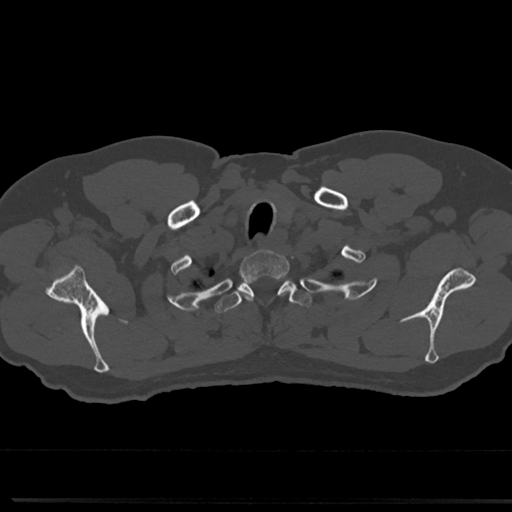
CT including the spine, one axial slice. Slice 651 of 817 in the series (ordered by position). Bone window (W 1800 / L 400 HU). 0.5 mm slice thickness. 512 × 512 image matrix. Patient: male, 61 years. From the clinical record (not read from this slice): primary cancer: prostate.
Structures marked on this image (semi-automatically segmented with operator editing):
- T1 vertebra: bounding box (x1, y1, x2, y2) in pixels: (242, 251, 287, 275)
- T2 vertebra: (222, 274, 306, 319)